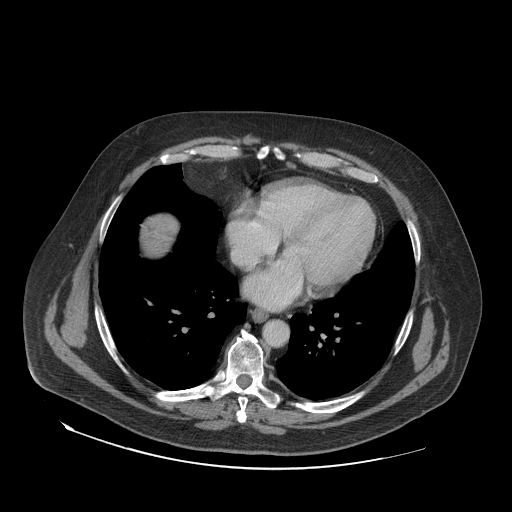
Contrast-enhanced abdominal CT (liver protocol), one axial slice. Slice 76 of 79 in the series (ordered by position). Soft-tissue window (W 400 / L 40 HU). 512 × 512 image matrix, field of view 480 × 480 mm. Case-level facts recorded for this patient, not image findings: diagnosis: hepatocellular carcinoma (patient treated with transarterial chemoembolisation; whether this scan precedes or follows treatment is not stated here); TNM stage (as recorded): Stage-IVA; Child-Pugh class: A; tumour differentiation: well differentiated; tumour nodularity: multinodular.
Annotated regions visible in this slice (semi-automatic segmentation, software-assisted and operator-edited):
- liver parenchyma outside the tumour (the mass and vessels are separate outlines, so this box may not span the whole liver): bounding box [x1, y1, x2, y2] px = [142, 215, 178, 256]